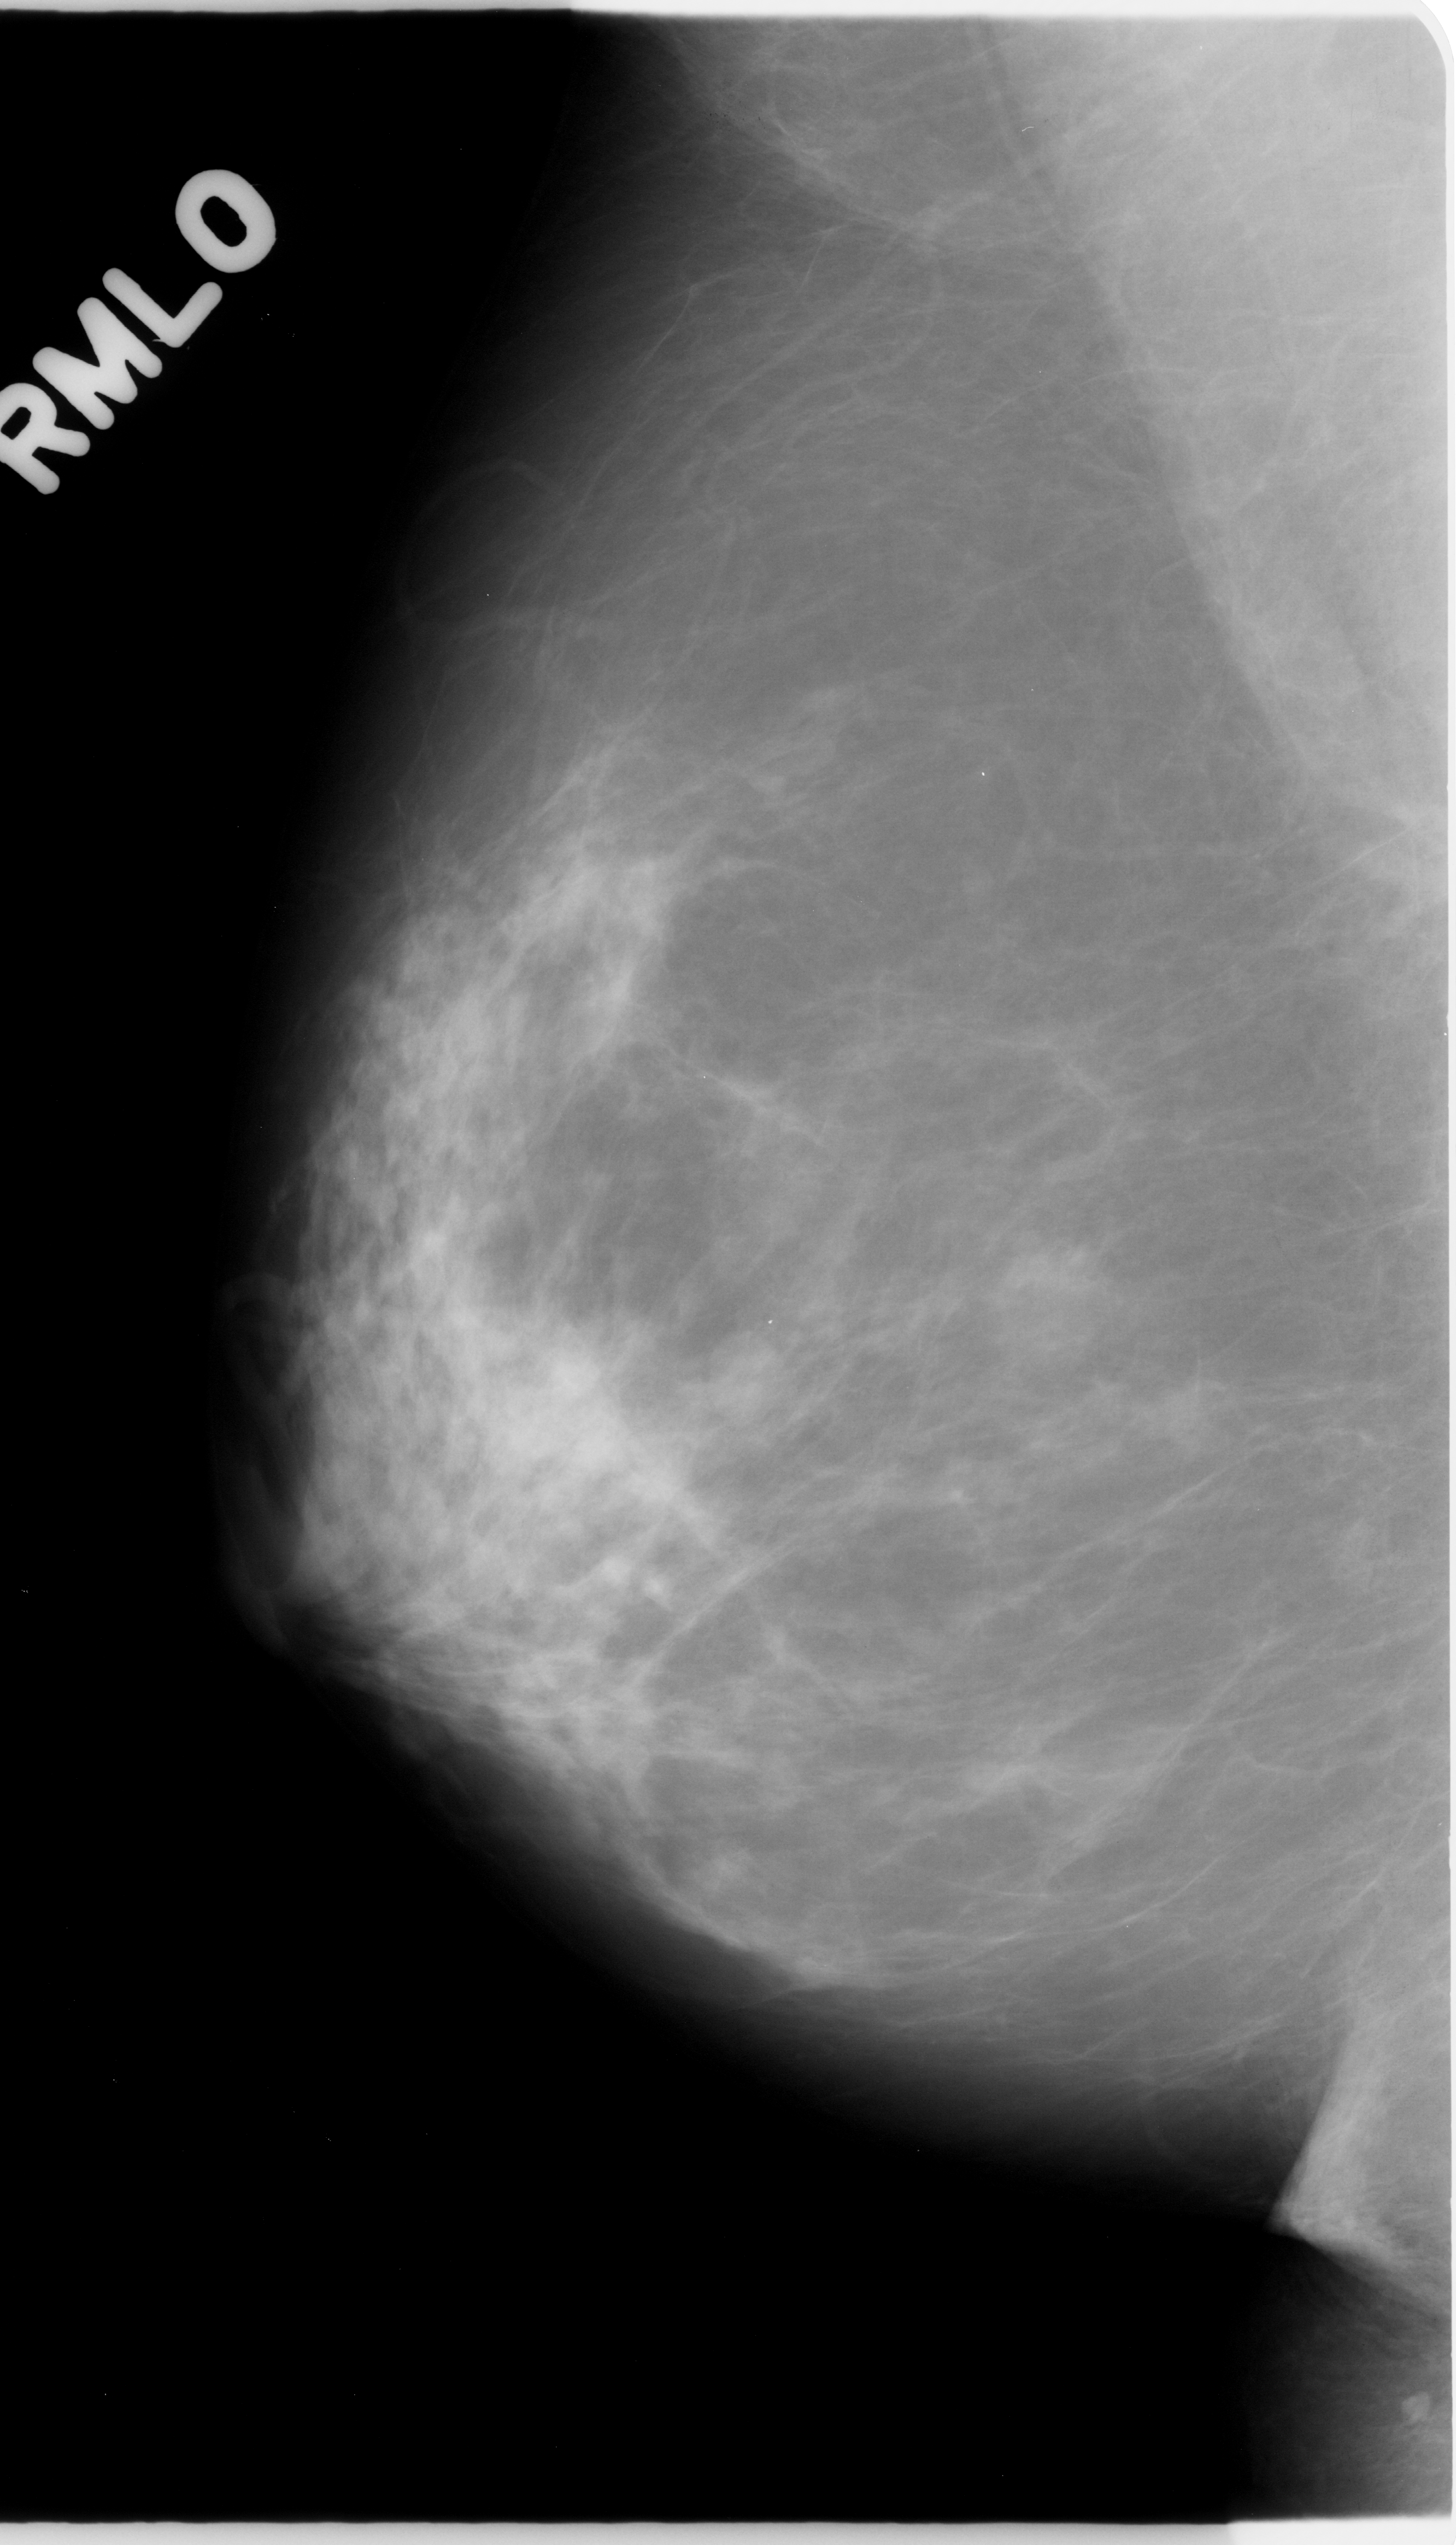
Scanned film-screen mammogram. Right breast. Mediolateral oblique (MLO) view. 1456 × 2545 image matrix.
Expert-marked regions of interest on this image (one box per marked abnormality):
- mass, shape oval, margins circumscribed; BI-RADS assessment category 3; pathology result (as recorded, not read from the image): benign: bounding box (x1, y1, x2, y2) in pixels: (673, 1322, 808, 1457)